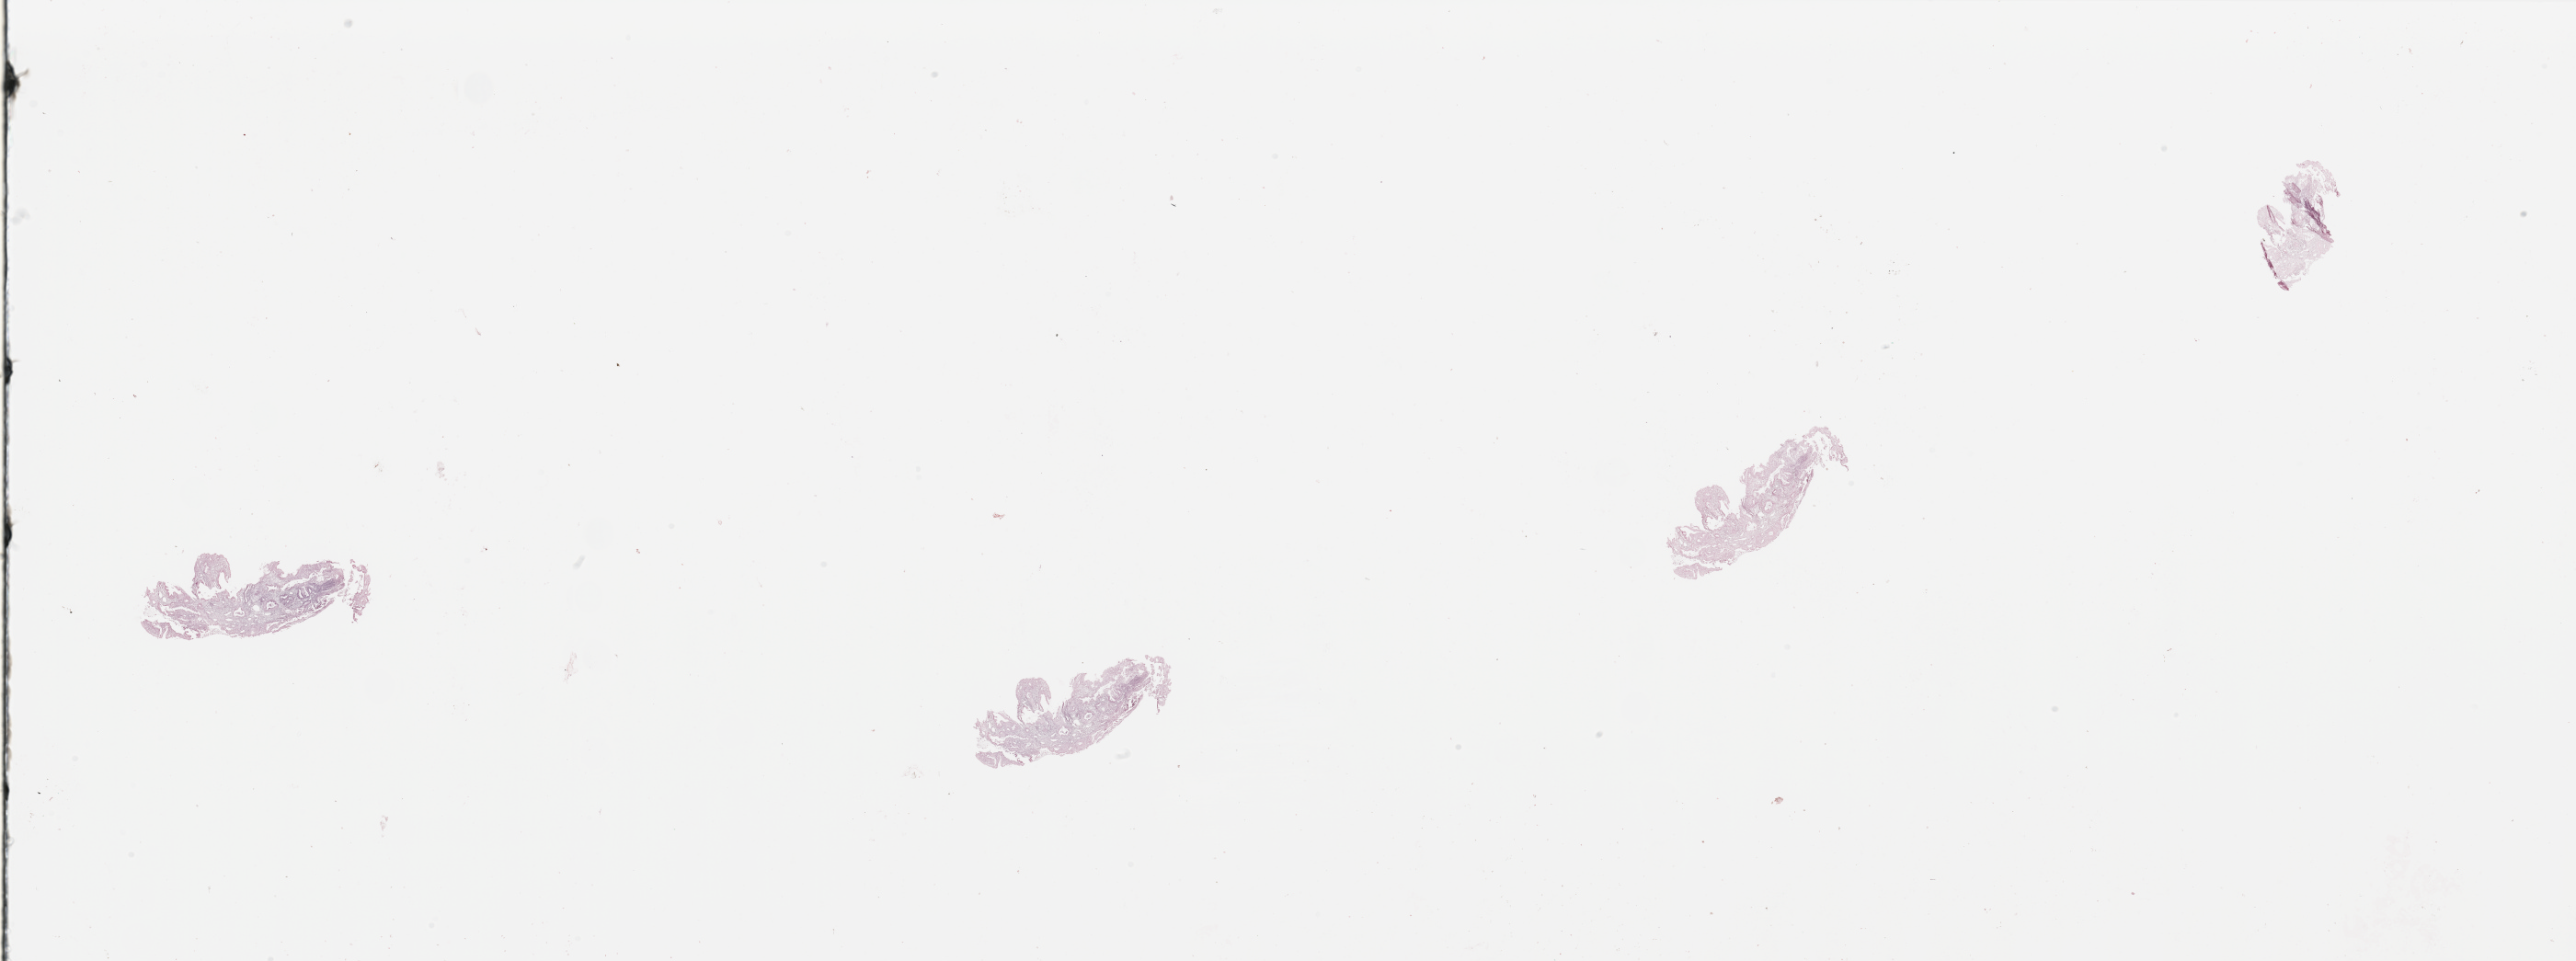
Whole-slide histology image, H&E-stained, a low-resolution overview of the entire scanned area, about 44.3 x 16.5 mm. Uterus, tumour tissue. Female, 67 y/o.
Diagnosis: Endometrioid adenocarcinoma, NOS.